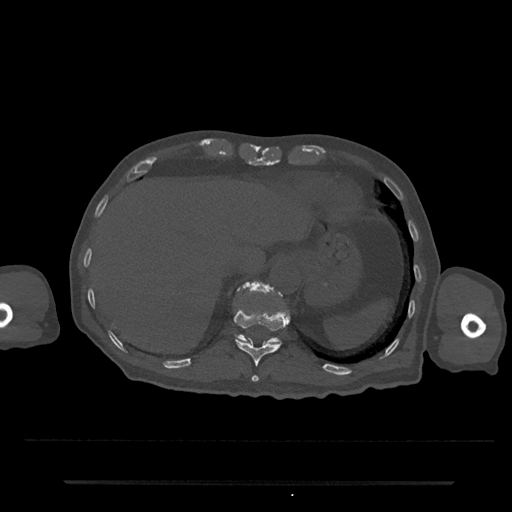
CT including the spine, one axial slice; position 242 of 797 along the scan axis; reconstruction kernel Br40s/3; 120 kVp; bone window (W 1800 / L 400 HU); 0.5 mm slice thickness; 512 × 512 image matrix. Patient: male, 74 years. Case-level facts recorded for this patient, not image findings: primary cancer: prostate.
Outlined on this slice (semi-automatically segmented with operator editing):
- T11 vertebra: box from (x=234, y=310) to (x=289, y=382) px
- T12 vertebra: (x=236, y=283)–(x=280, y=344)